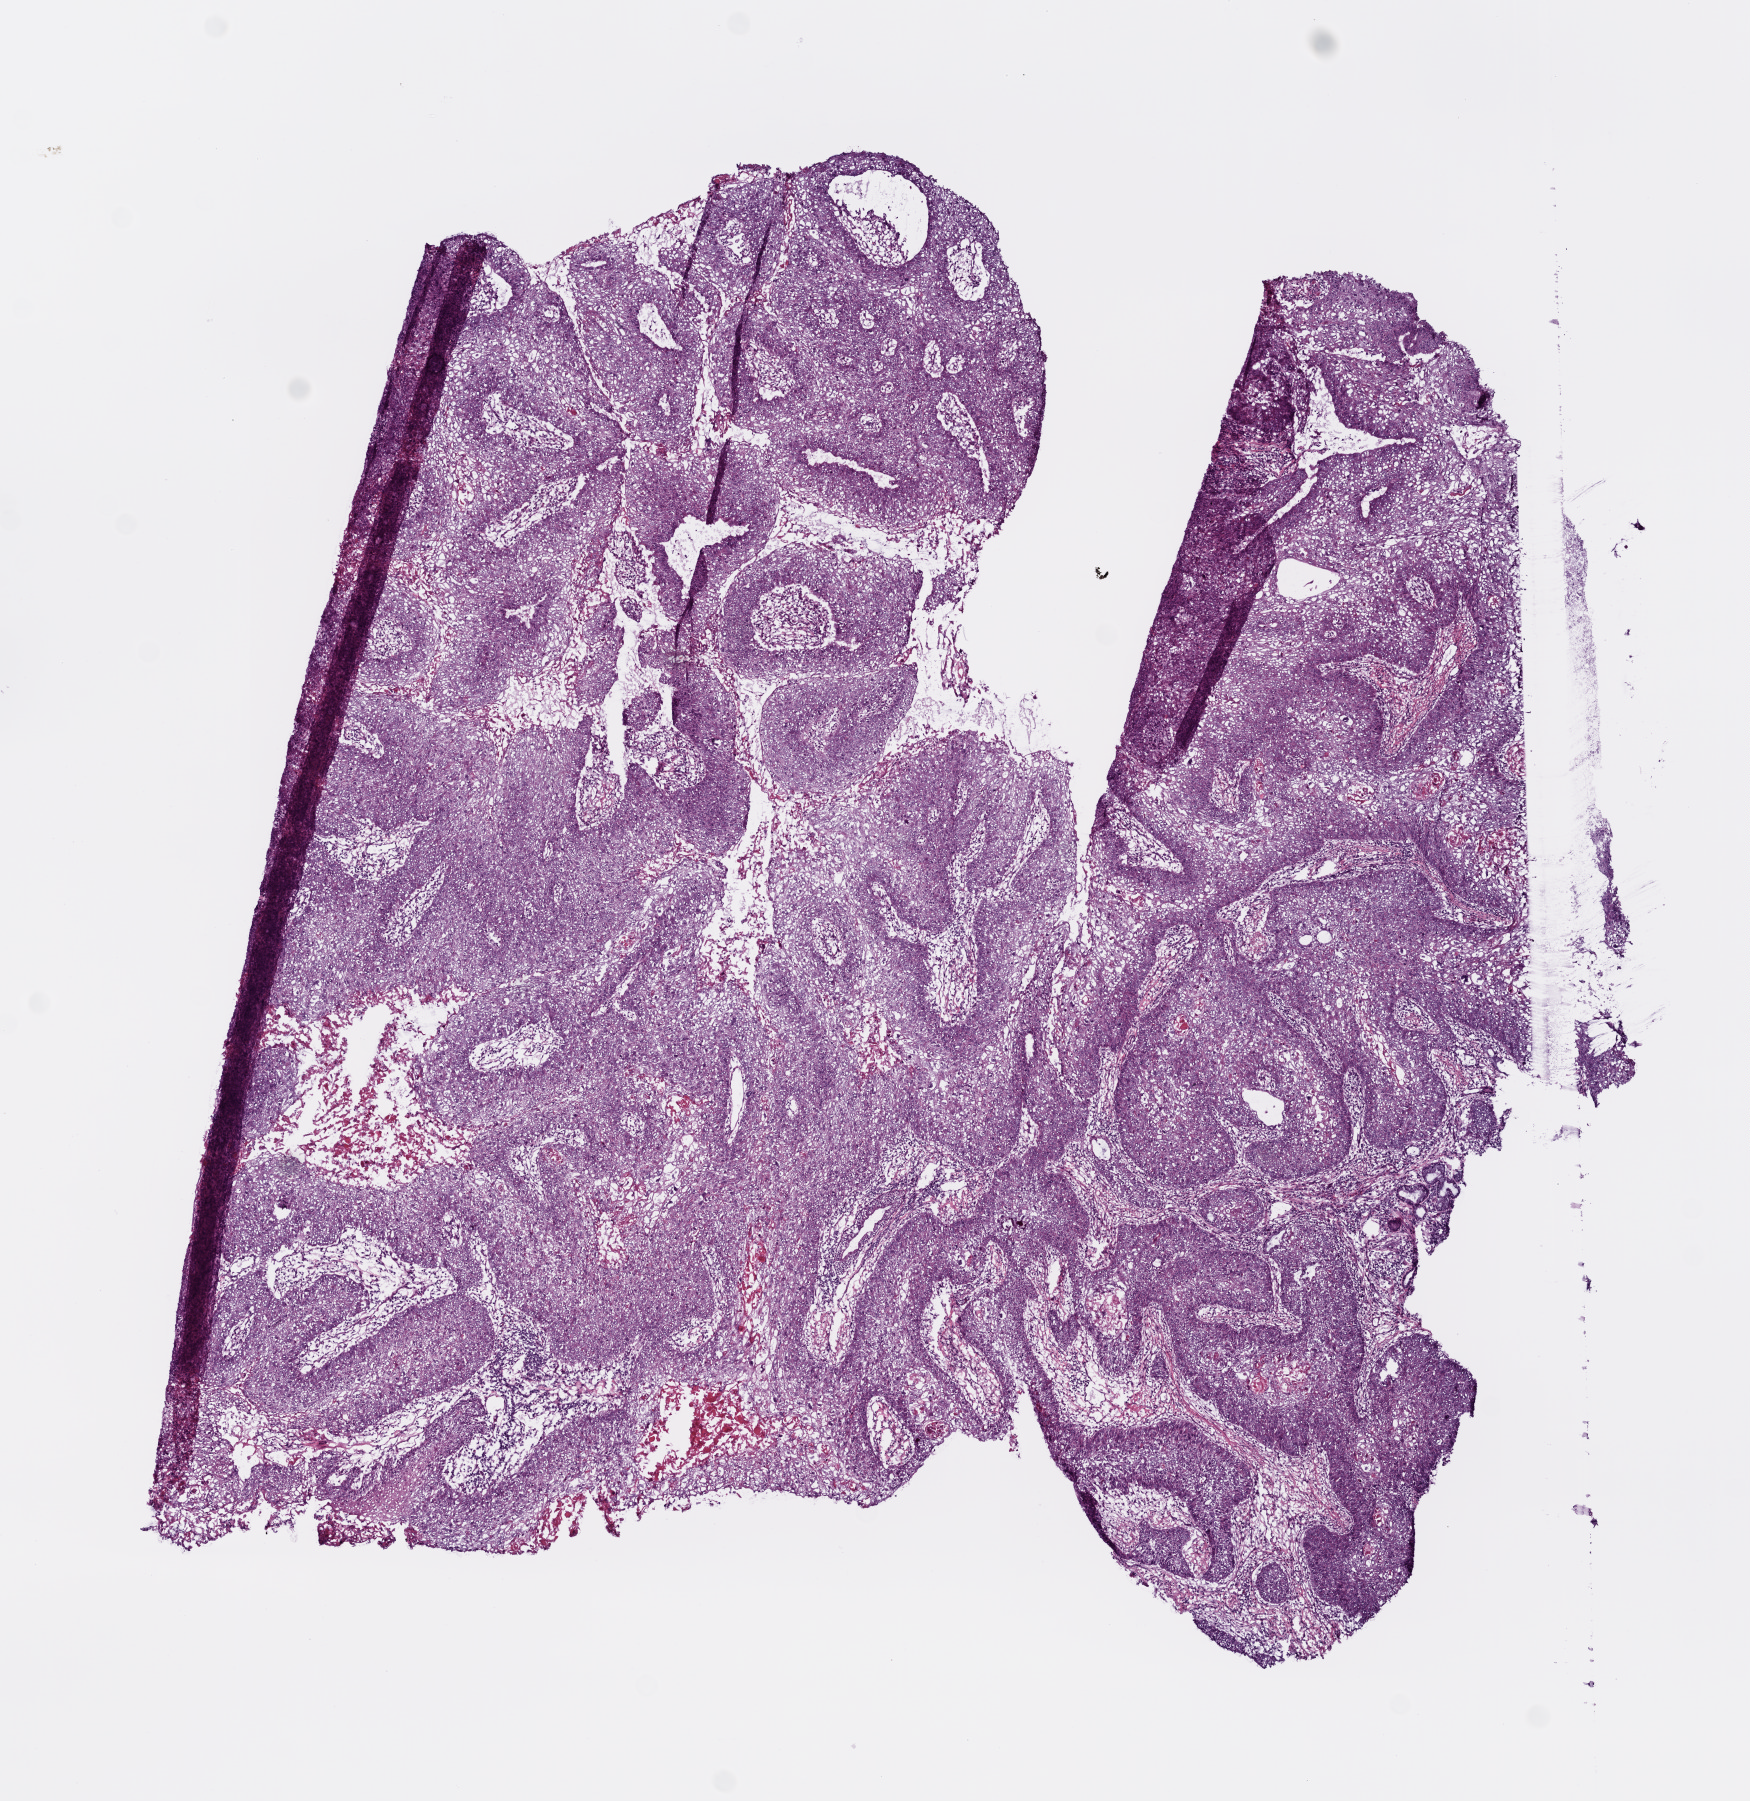
Whole-slide histology image, H&E-stained, low-resolution overview of the scanned area, about 7.0 x 7.2 mm. Frozen section from the bottom of the tissue portion. Primary tumour sample from the head and neck. Patient: male, age at initial diagnosis 54 years.
Histologic diagnosis: Squamous cell carcinoma, NOS (larynx, NOS).